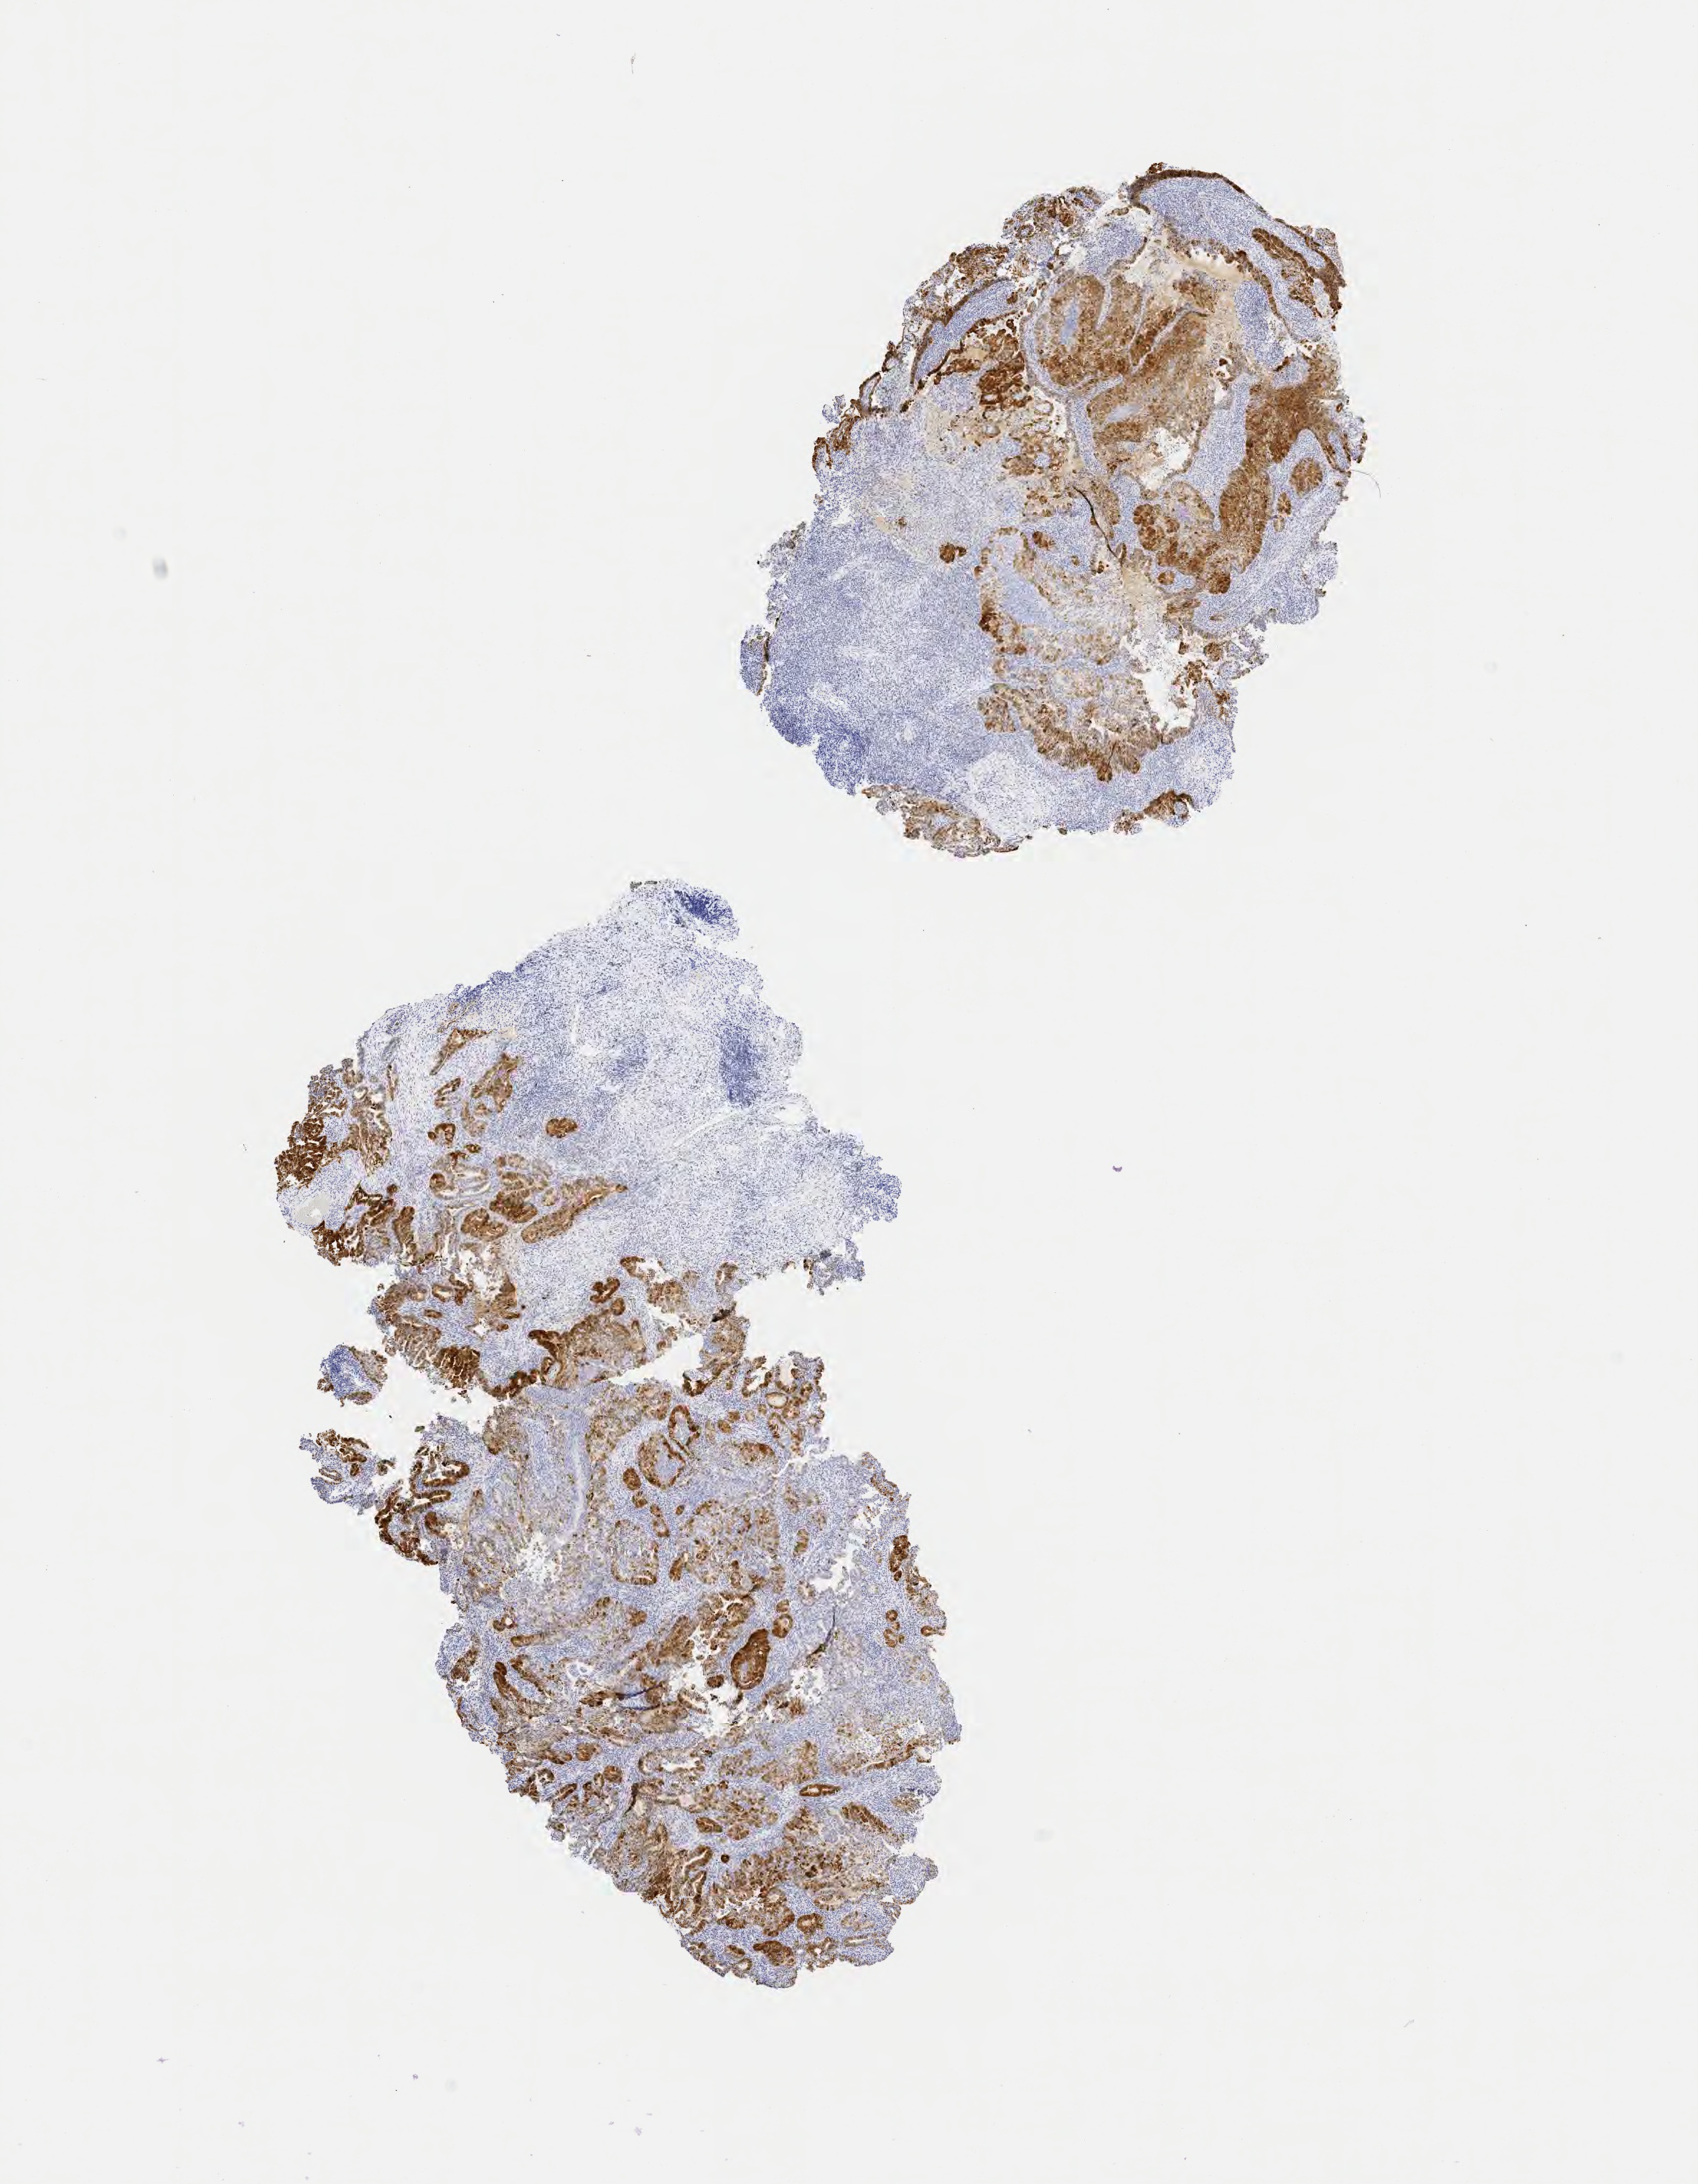
IHC for p16 (p16INK4a), whole-slide image — a low-resolution overview of the entire scanned area, about 9.6 x 12.3 mm, specimen: tumor tissue, anatomic site: cervix. Patient female; aged 48.
Histologic diagnosis: Adenocarcinoma, NOS.